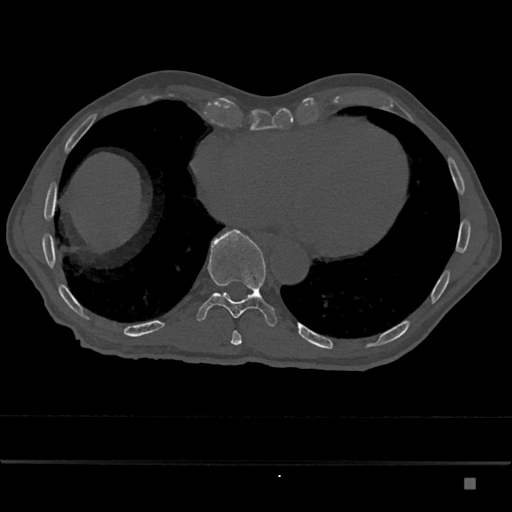
CT including the spine, one axial slice. Position 744 of 797 along the scan axis. Reconstruction kernel Br40s/3. Bone window (W 1800 / L 400 HU). 512 × 512 image matrix, field of view 390 × 390 mm. Male patient, age 72 years. Case-level facts recorded for this patient, not image findings: primary cancer: prostate.
Annotated regions visible in this slice (semi-automatically segmented with operator editing):
- T10 vertebra: bounding box <197,229,277,327> (left, top, right, bottom; pixels)
- T9 vertebra: <231,331,242,346>